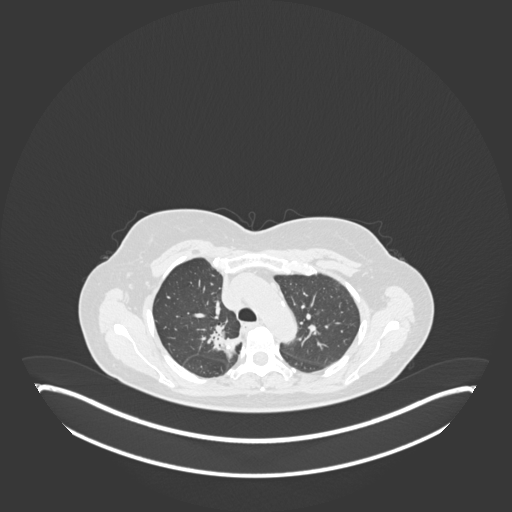
Chest CT, one axial slice; slice 129 of 181 in the series (ordered by position); reconstruction kernel B30f; 120 kVp; lung window (W 1500 / L -600 HU); 512 × 512 image matrix, field of view 500 × 500 mm. Patient: female, 65 years. From the clinical record (not read from this slice): clinical TNM (as recorded): T1b N0 M0; histopathological grade: G2.
Outlined on this slice (rectangle marked by the reading radiologist):
- lung tumour (recorded histology: adenocarcinoma): bounding box <208,329,240,359> (left, top, right, bottom; pixels)